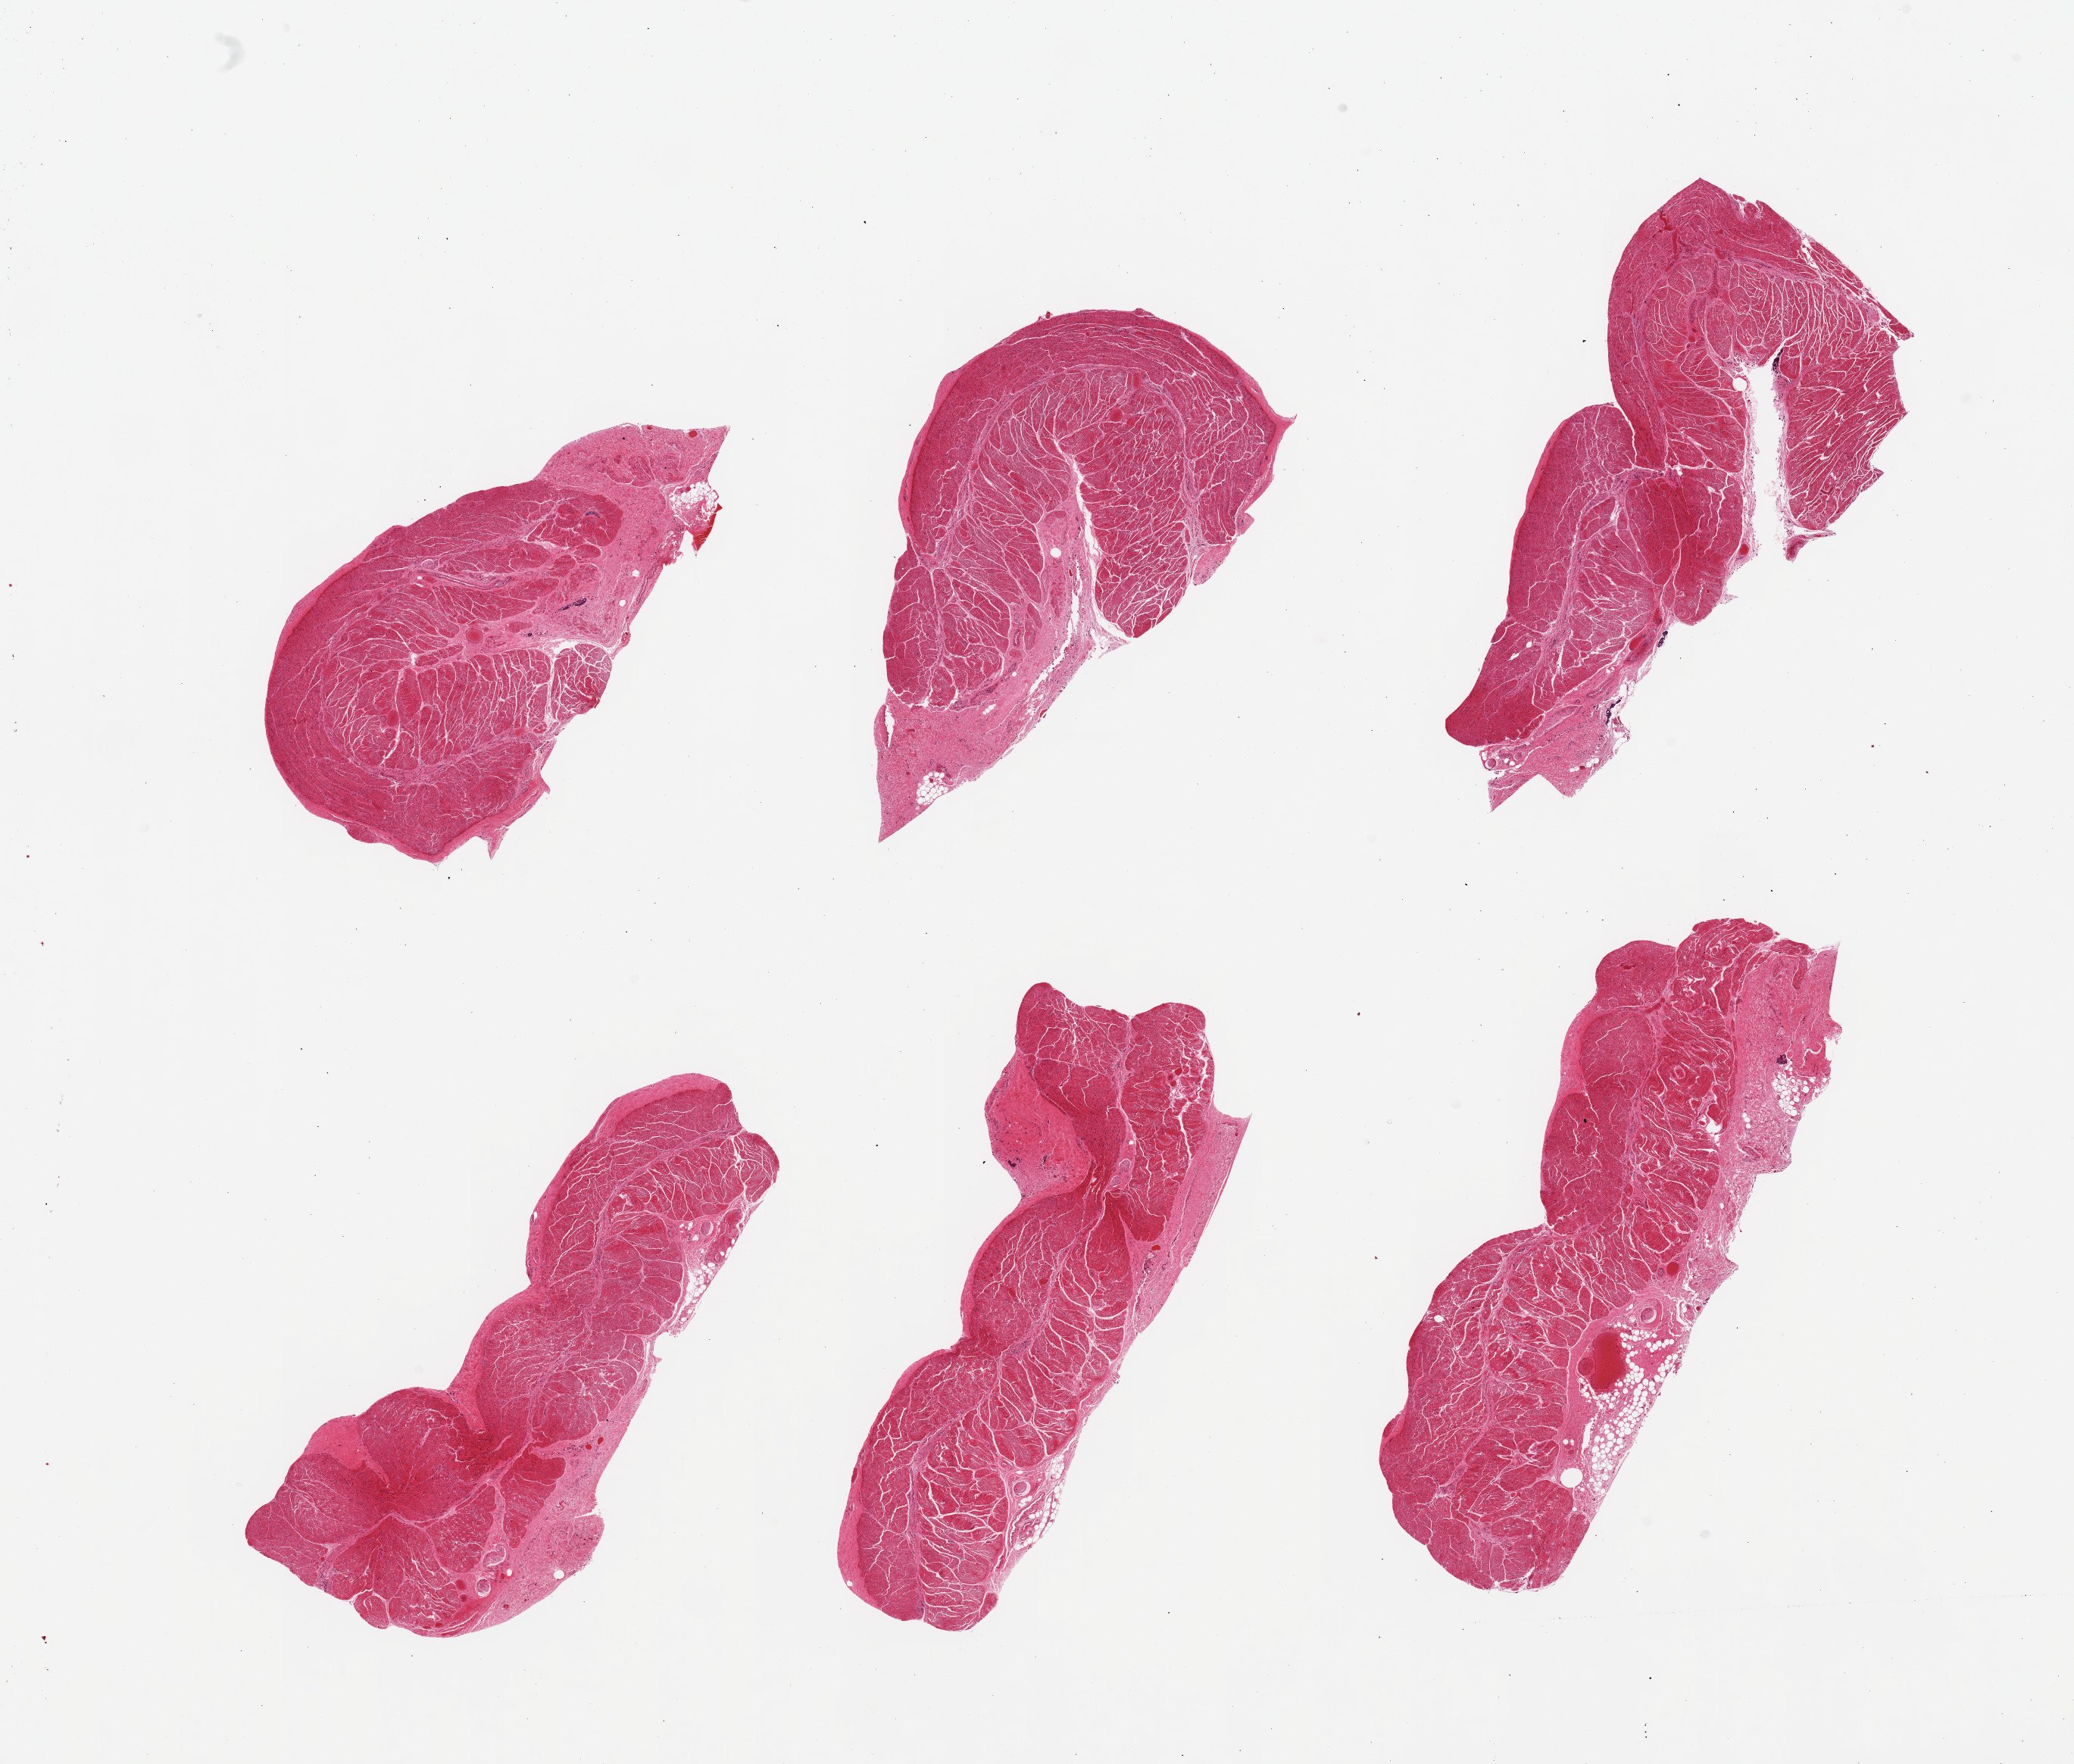
Whole-slide image, haematoxylin and eosin stain — shown as a low-resolution overview of the whole scanned area (about 21.7 x 18.4 mm, acquisition: 20x scan); PAXgene-fixed, paraffin-embedded tissue; target tissue: esophageal muscle; tissue donor sample. Female donor.
Pathologist's review note for this sample: 6 pieces, confirmed target muscularis.